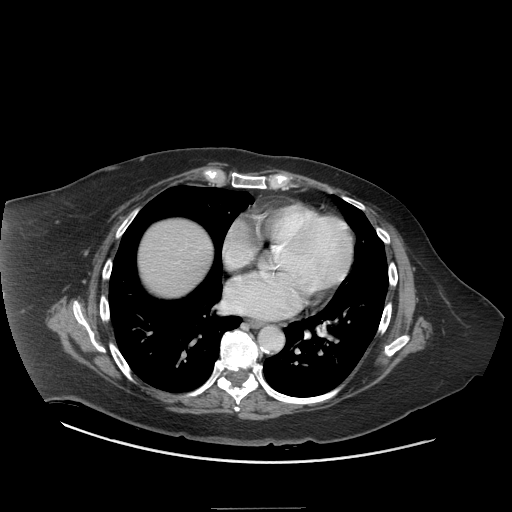
Contrast-enhanced abdominal CT (liver protocol), one axial slice. Slice 74 of 81 in the series (ordered by position). Reconstruction kernel STANDARD. Soft-tissue window (W 400 / L 40 HU). 2.5 mm slice thickness. 512 × 512 image matrix, field of view 440 × 440 mm. Case-level facts recorded for this patient, not image findings: diagnosis: hepatocellular carcinoma (patient treated with transarterial chemoembolisation; whether this scan precedes or follows treatment is not stated here); TNM stage (as recorded): Stage-II; Child-Pugh class: A; tumour differentiation: moderately differentiated; tumour size: 1.7 cm.
Annotated regions visible in this slice (semi-automatic segmentation, software-assisted and operator-edited):
- liver parenchyma outside the tumour (the mass and vessels are separate outlines, so this box may not span the whole liver): box from (x=138, y=220) to (x=212, y=294) px